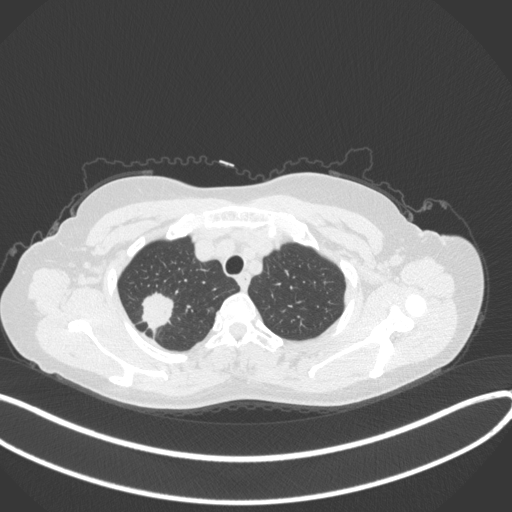
Chest CT, one axial slice. Position 309 of 342 along the scan axis. Reconstruction kernel B31f. 120 kVp. Lung window (W 1500 / L -600 HU). 1 mm slice thickness. 512 × 512 image matrix. Female patient, age 50 years. From the clinical record (not read from this slice): clinical TNM (as recorded): T1c N0 M0.
Structures marked on this image (bounding box drawn by a radiologist):
- lung tumour (recorded histology: adenocarcinoma): bounding box (x1, y1, x2, y2) in pixels: (140, 292, 175, 333)